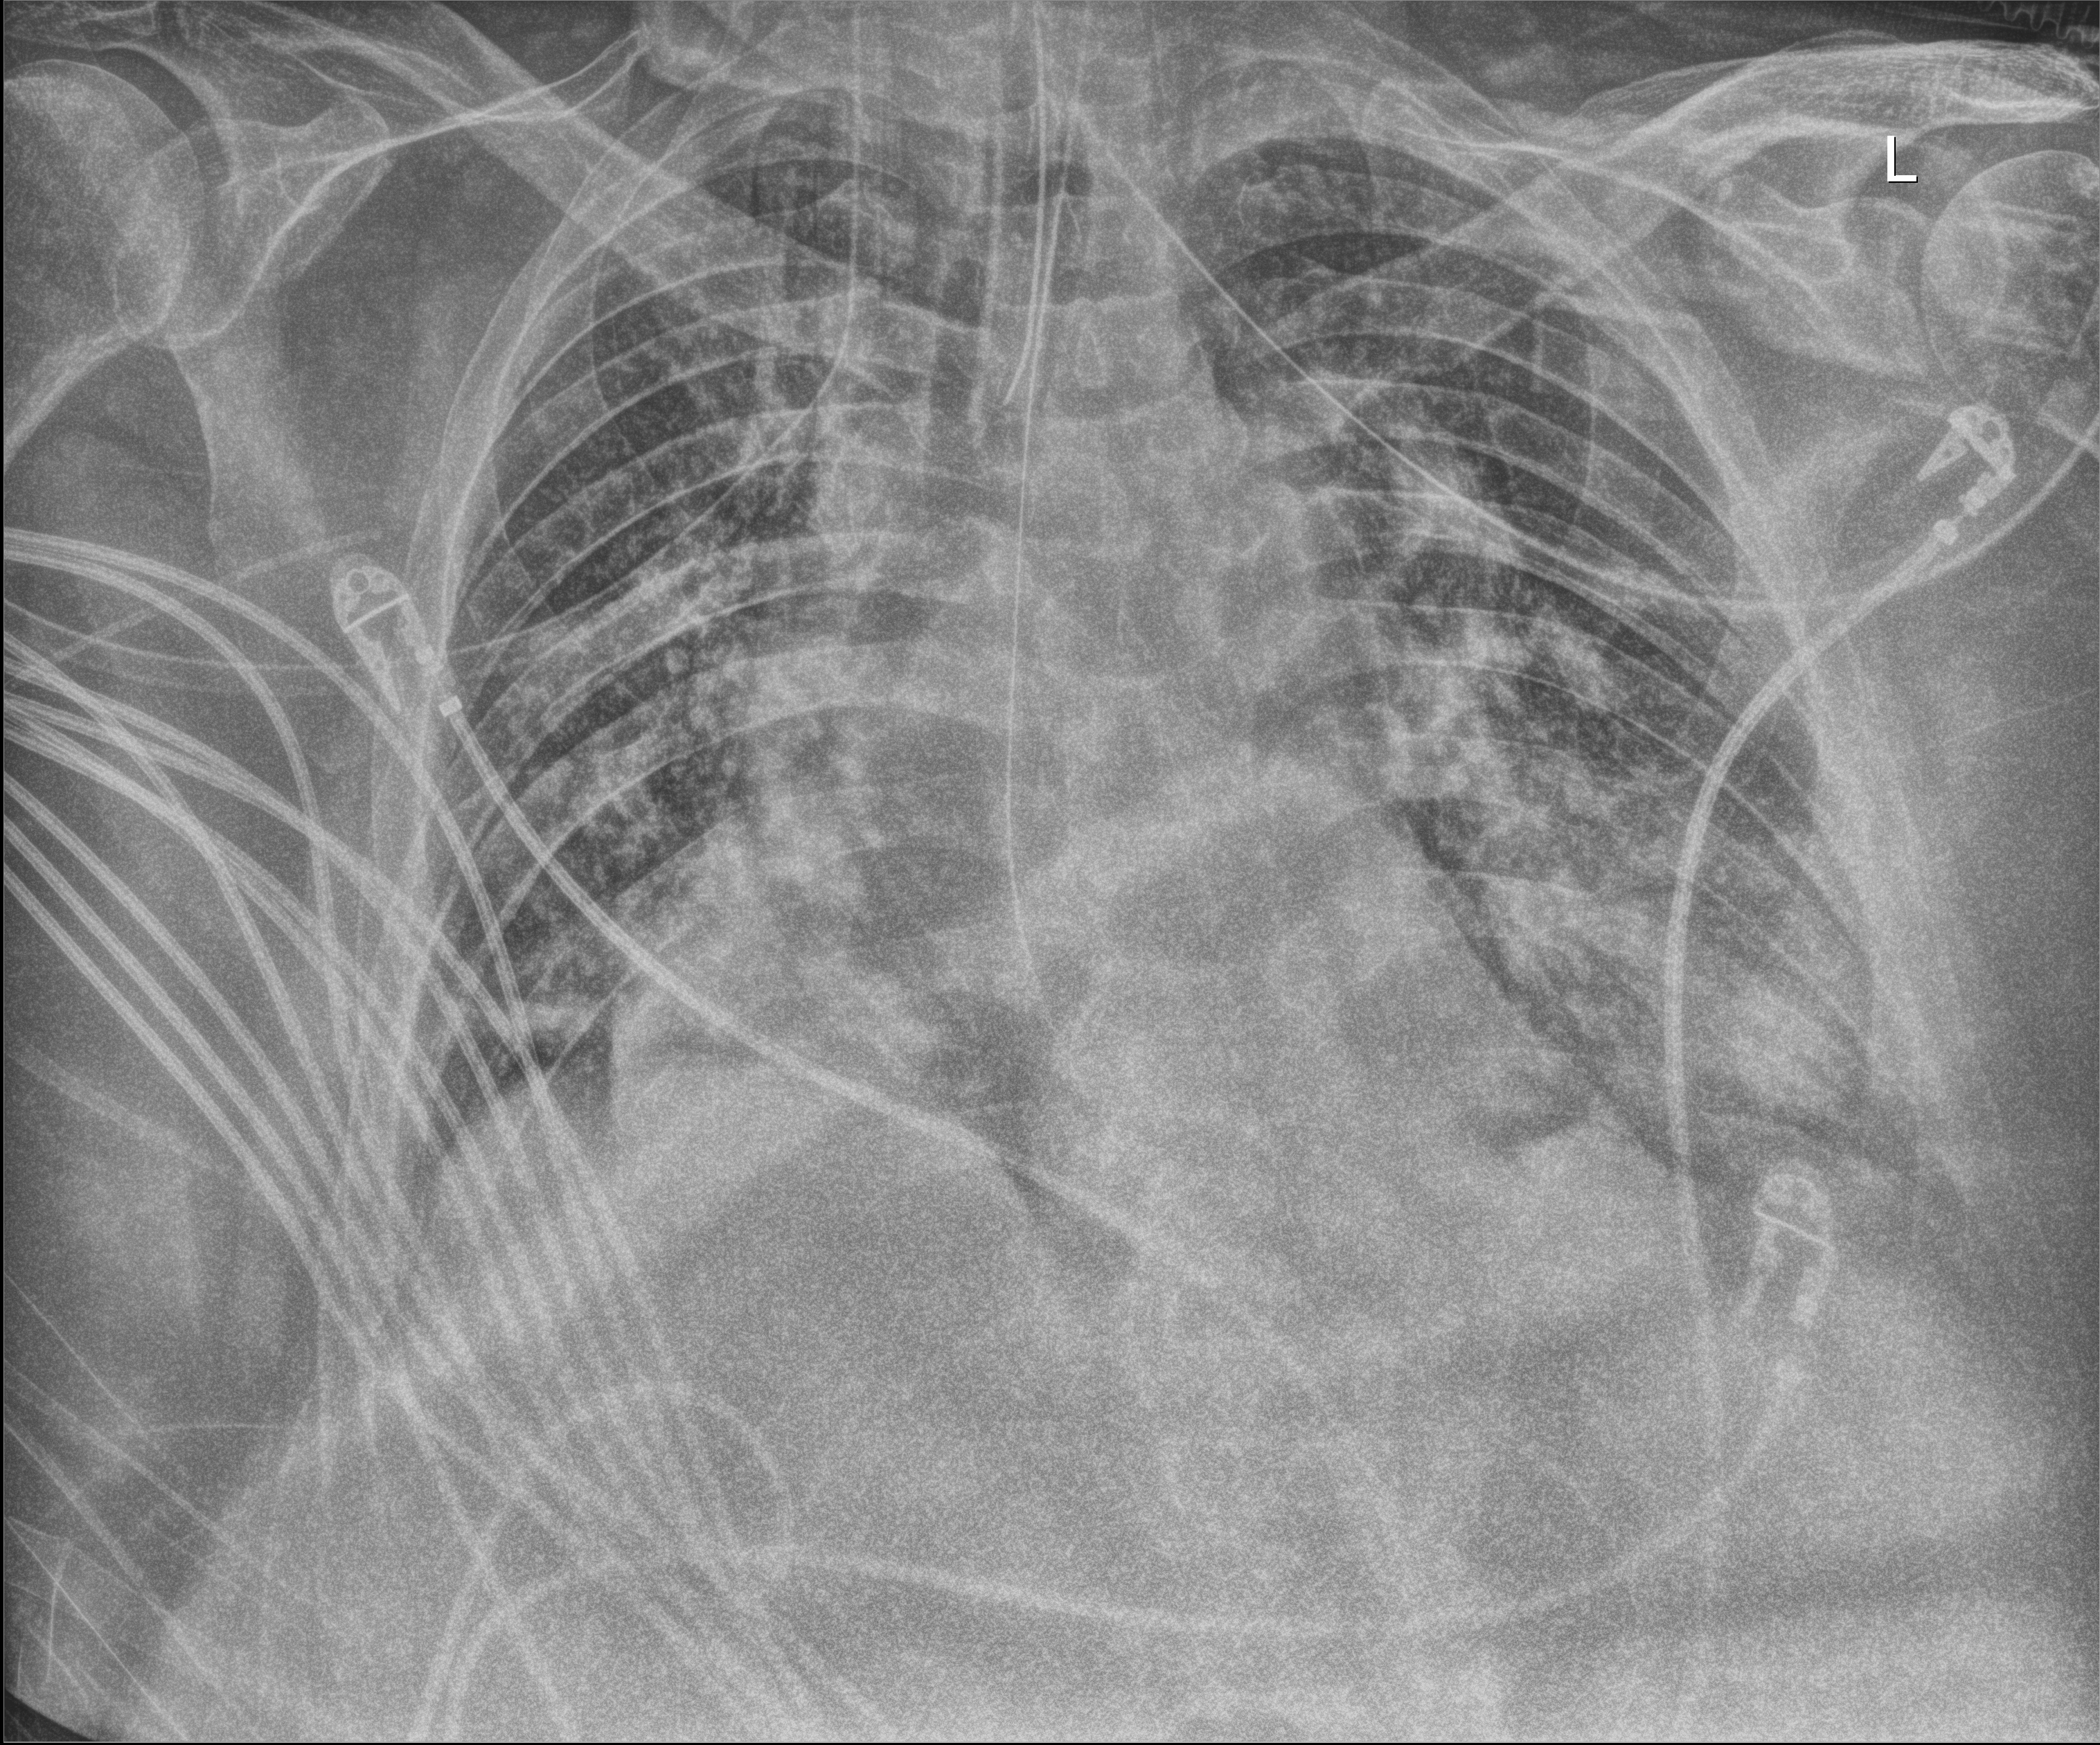
Chest radiograph; anteroposterior (AP) projection. Patient hospitalised with COVID-19; male, aged 60–74 years.
Hospital-stay facts (about this admission, not read from this image; timing relative to this image not recorded): length of hospital stay: 10 days; diabetes (admission record): no; mechanically ventilated during this hospital stay: yes.